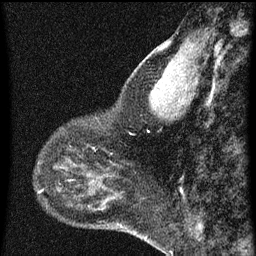
Breast MRI (dynamic contrast-enhanced), one sagittal slice. Slice 21 of 60 in the series (ordered by position). Dynamic contrast-enhanced series, image 2 of 3 at this slice position (ordered by acquisition). 1.5 T. TE 4.2 ms, TR 8 ms. 256 × 256 image matrix, field of view 180 × 180 mm. Patient: female, 44 years.
Structures marked on this image (semi-automatic segmentation, software-assisted and operator-edited):
- analysis volume of interest (the breast-tissue region the enhancement analysis was run in; not a lesion): bounding box [x1, y1, x2, y2] px = [49, 128, 95, 169]
- tumour enhancement mask (voxels above the 70 % enhancement threshold inside the analysis volume of interest): [69, 146, 95, 167]